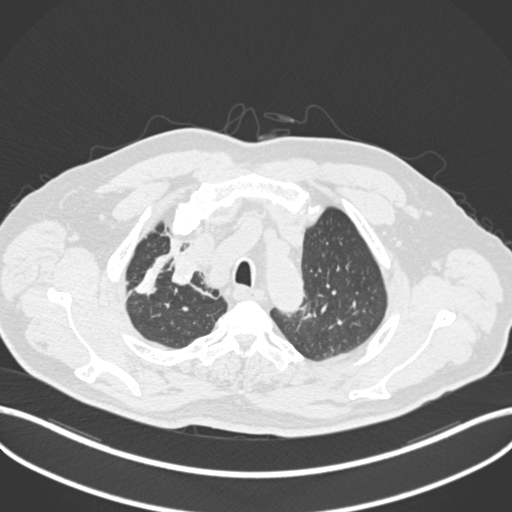
Chest CT, one axial slice; position 168 of 255 along the scan axis; reconstruction kernel B30f; 120 kVp; lung window (W 1500 / L -600 HU); 1 mm slice thickness; 512 × 512 image matrix. Male patient, age 60 years. Case-level facts recorded for this patient, not image findings: clinical TNM (as recorded): T1b N1 M0.
Structures marked on this image (rectangle marked by the reading radiologist):
- lung tumour (recorded histology: squamous cell carcinoma): bounding box [x1, y1, x2, y2] px = [163, 244, 202, 294]